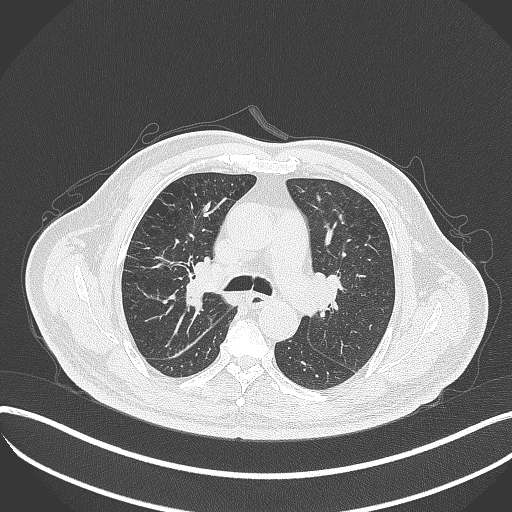
Chest CT, one axial slice; position 235 of 401 along the scan axis; 120 kVp; lung window (W 1500 / L -600 HU); 1 mm slice thickness; 512 × 512 image matrix, field of view 400 × 400 mm. Male patient, age 72 years. Case-level facts recorded for this patient, not image findings: clinical TNM (as recorded): T1c N0 M0.
Outlined on this slice (rectangle marked by the reading radiologist):
- lung tumour (recorded histology: squamous cell carcinoma): box from (x=171, y=255) to (x=205, y=311) px